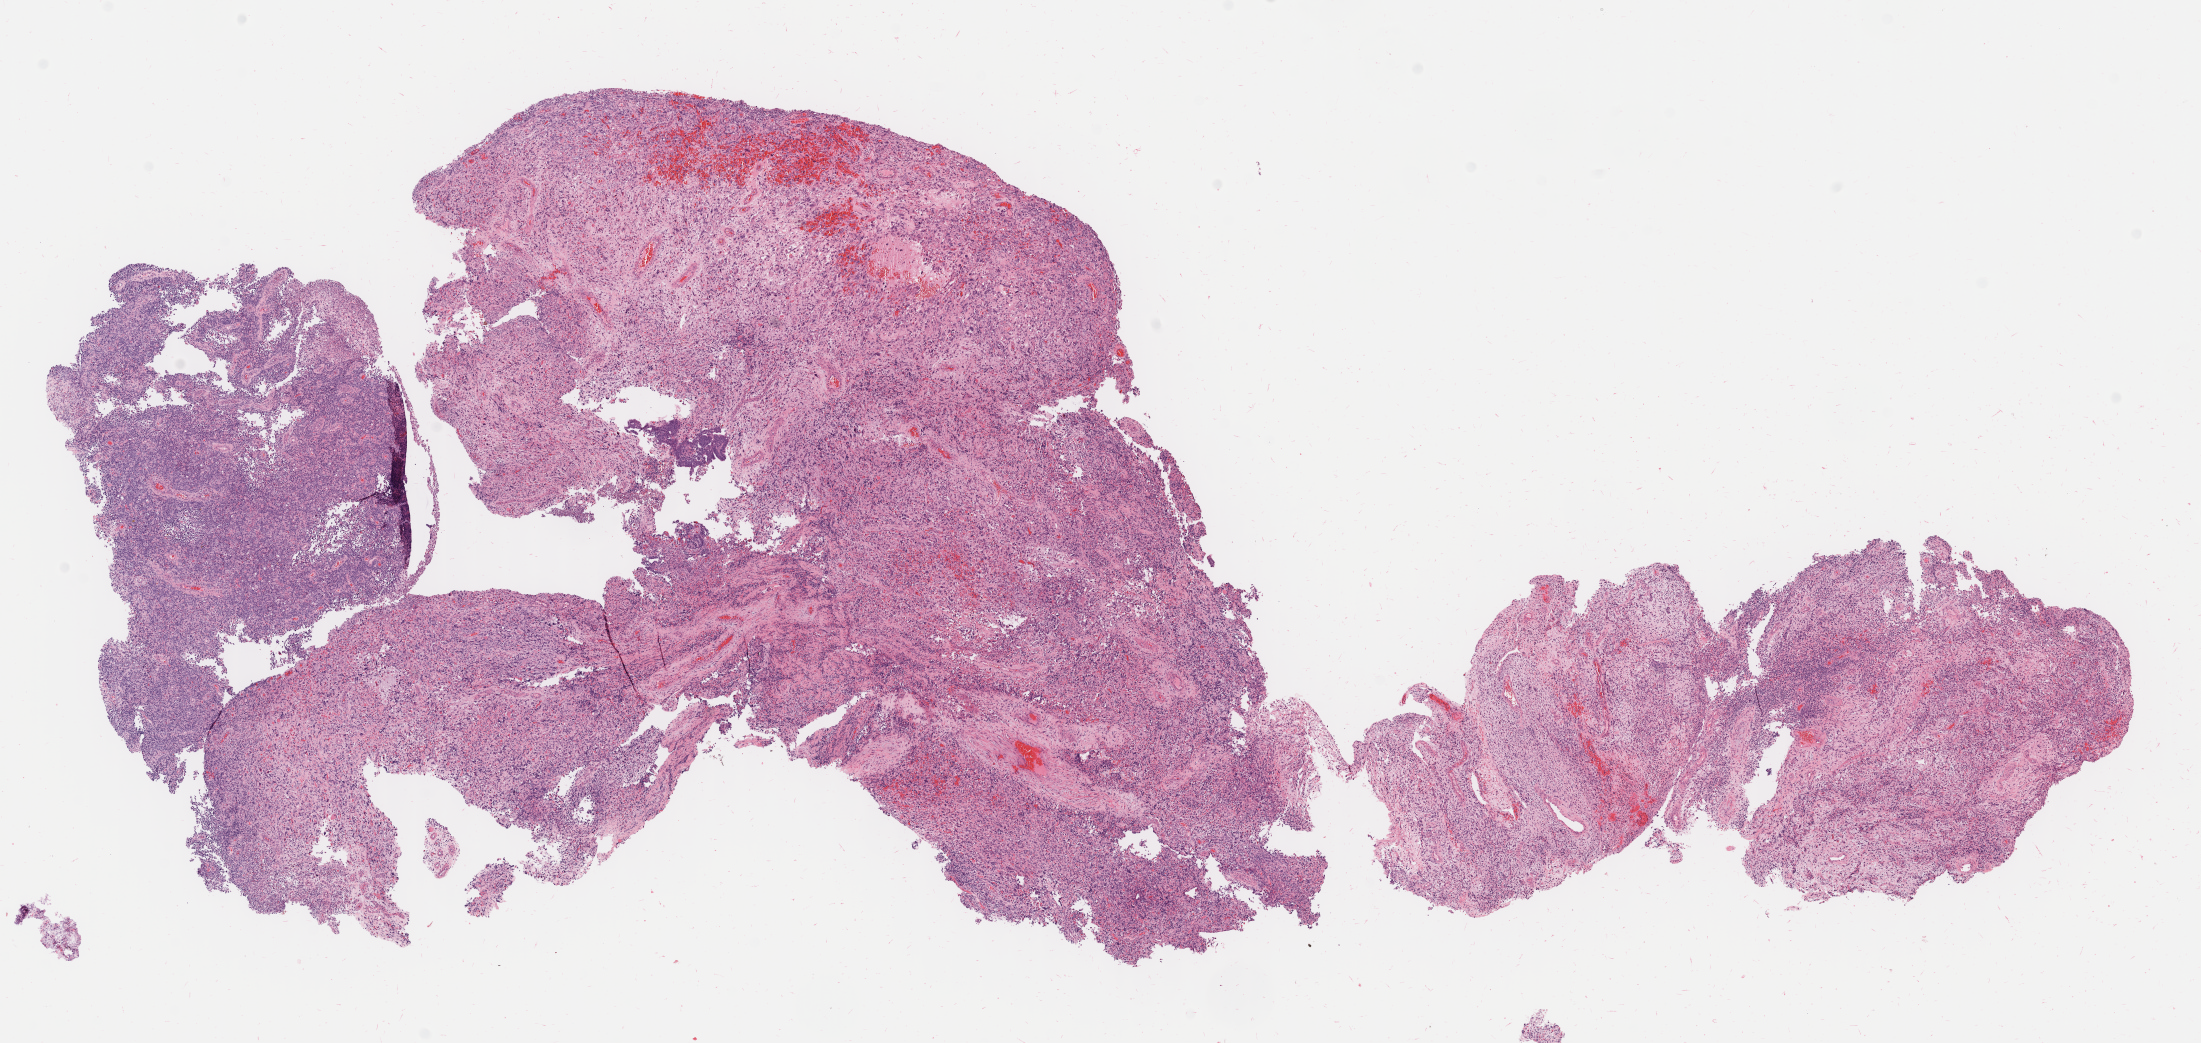
Haematoxylin and eosin whole-slide image — low-resolution overview of the scanned area, about 17.5 x 8.3 mm, specimen: tumor tissue, anatomic site: cervix. Female patient, aged 48.
Histologic diagnosis: Squamous cell carcinoma, NOS.